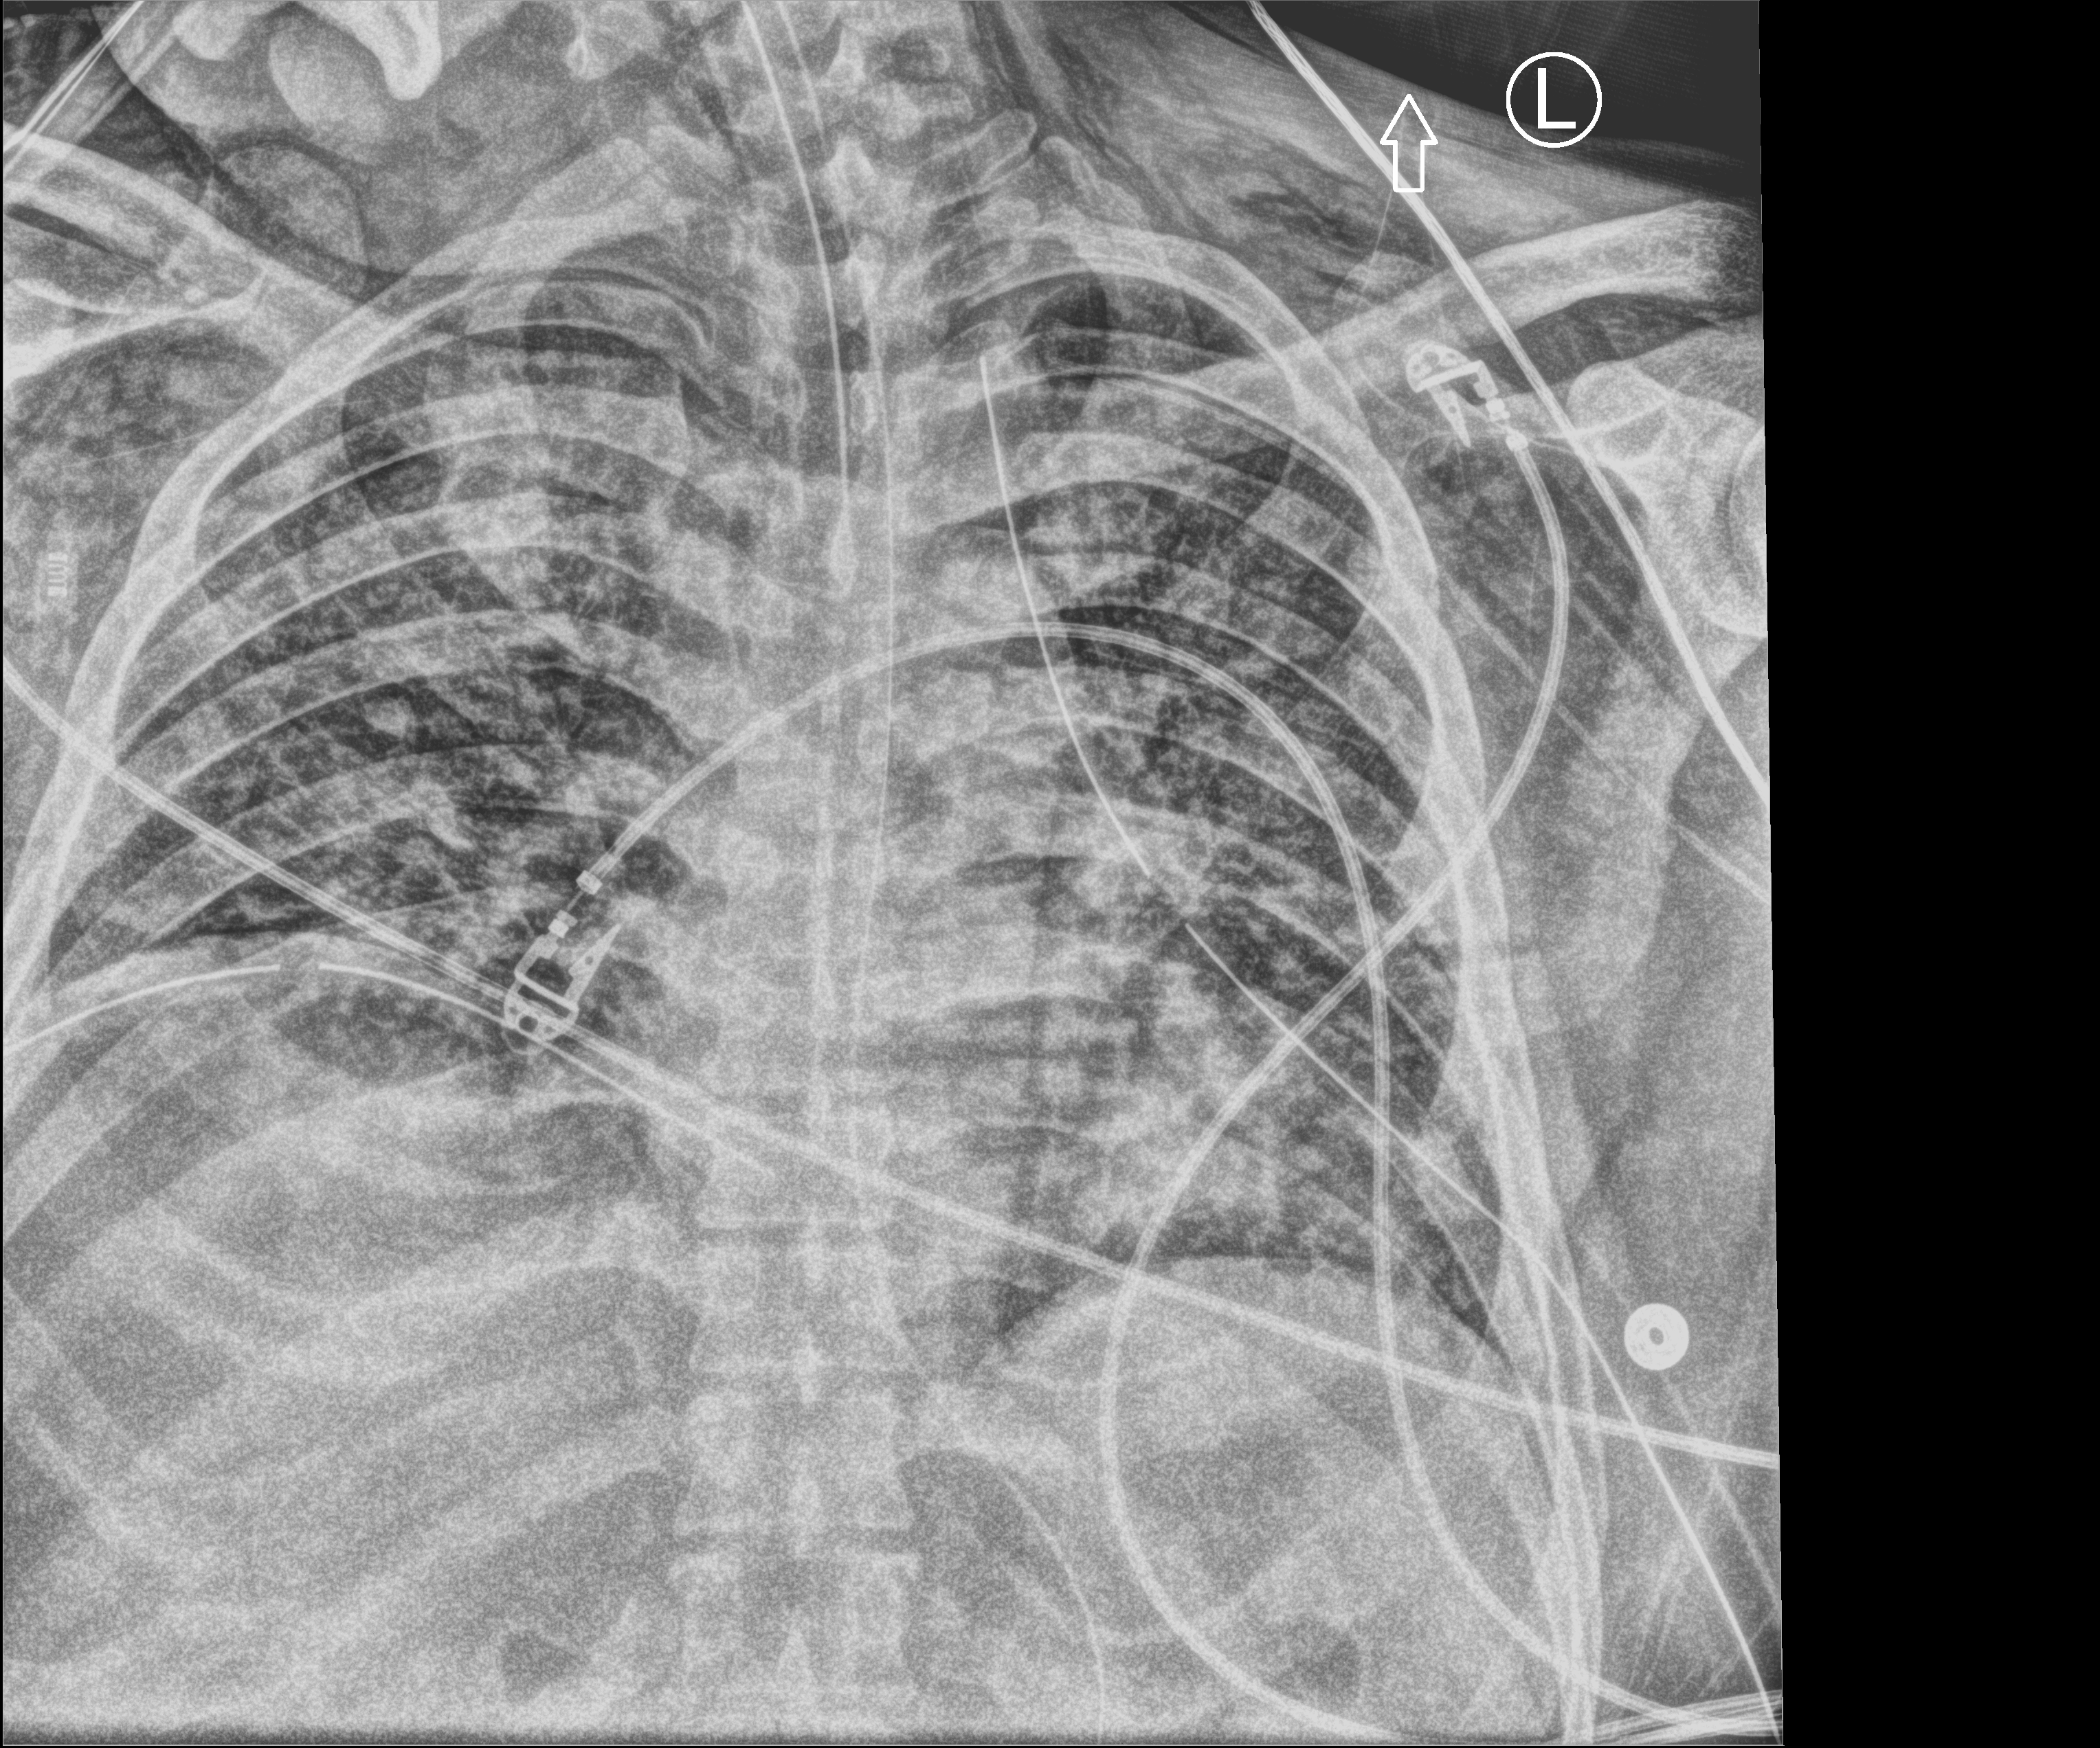
Bedside chest radiograph (computed radiography). Male patient hospitalised with COVID-19, age 18–59 years.
Admission-level facts for this patient (not findings on this image; timing relative to this image not recorded):
- mechanically ventilated during this hospital stay: yes